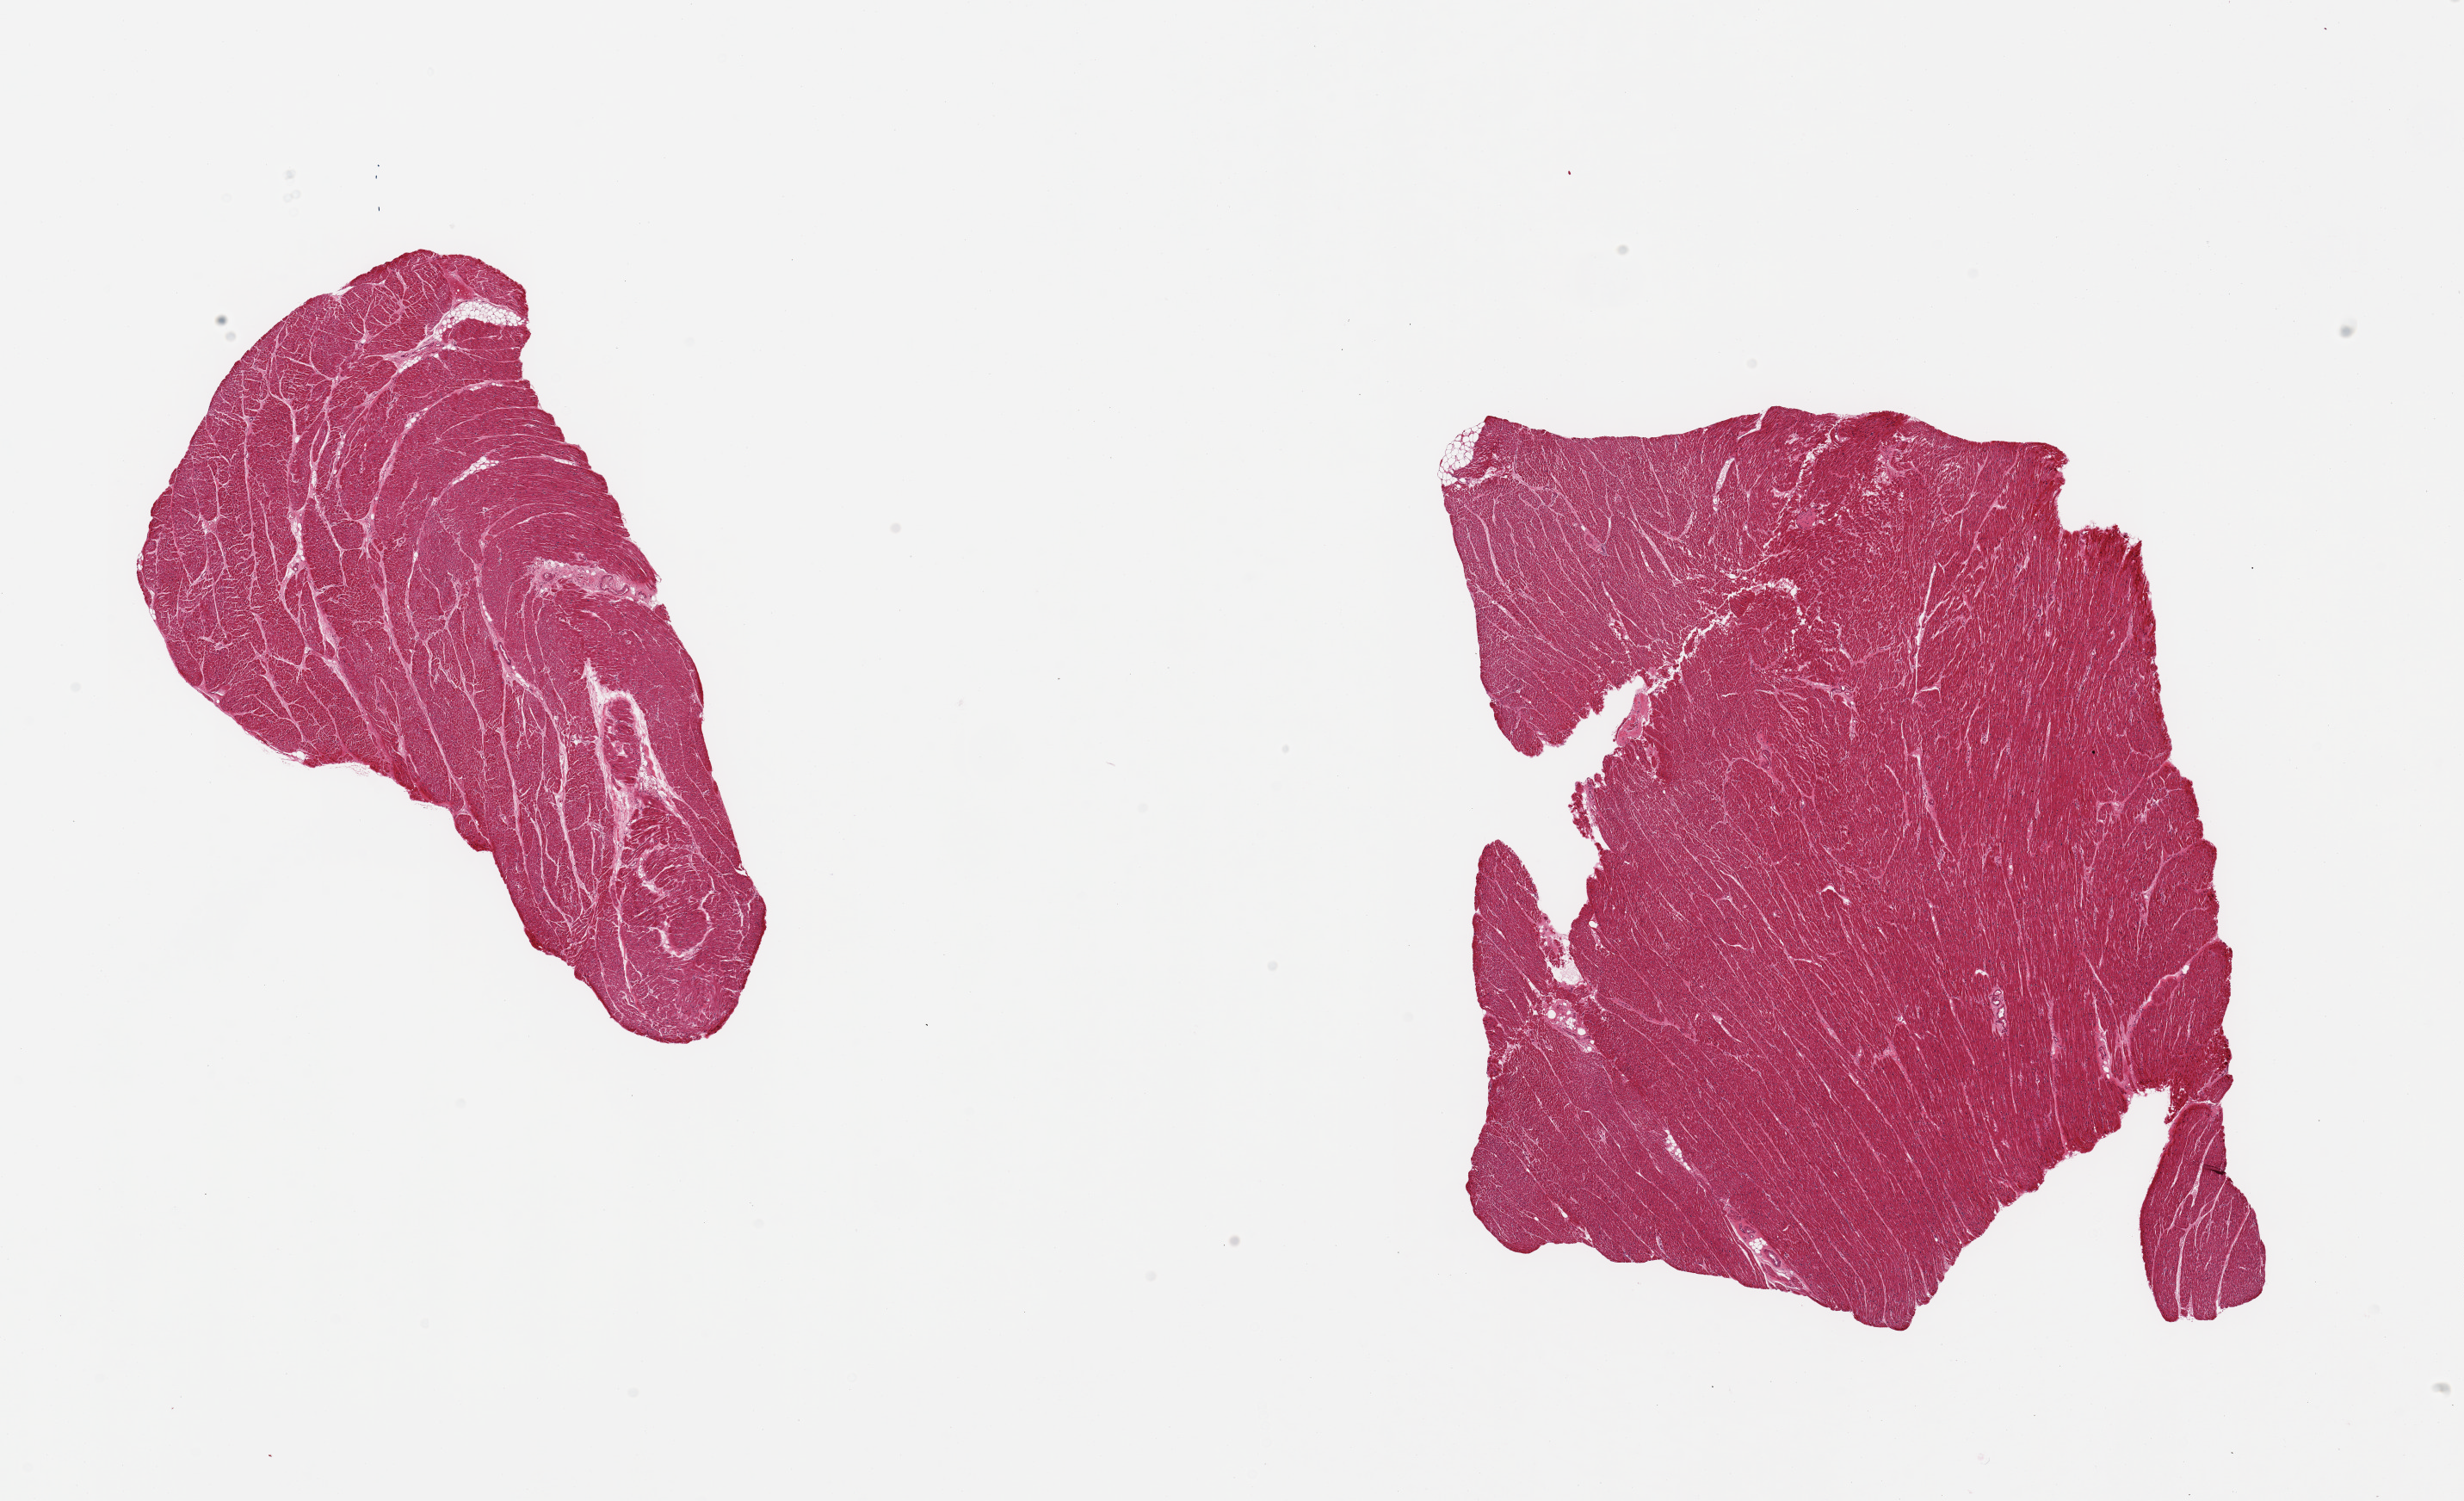
H&E whole-slide image, whole scanned area (about 22.6 x 13.8 mm) shown as a low-resolution overview, PAXgene-fixed paraffin-embedded (PFPE) section, section of heart (target tissue), tissue donor sample. Donor sex: male.
Pathologist's review note for this sample: 2 pieces; enlarged nuclei consistent with hypertrophy.